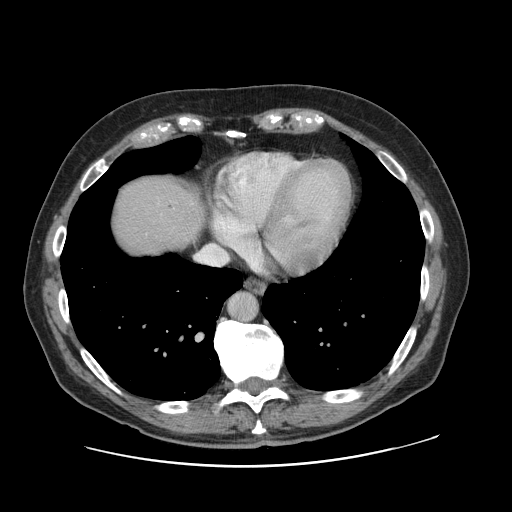
Contrast-enhanced abdominal CT, one axial slice. Position 114 of 138 along the scan axis. 120 kVp. Intravenous contrast given. Soft-tissue window (W 400 / L 40 HU). 512 × 512 image matrix, field of view 402 × 402 mm. Male patient, age 71 years. Case-level facts recorded for this patient, not image findings: diagnosis: colorectal cancer liver metastases, imaged before liver resection; multiple liver metastases: no; largest metastasis: 3.3 cm; disease in both lobes: no.
Annotated regions visible in this slice (outlined manually by an expert reader):
- liver: box from (x=110, y=174) to (x=204, y=259) px
- planned liver remnant (the part of the liver to remain after resection): (x=110, y=175)–(x=202, y=259)